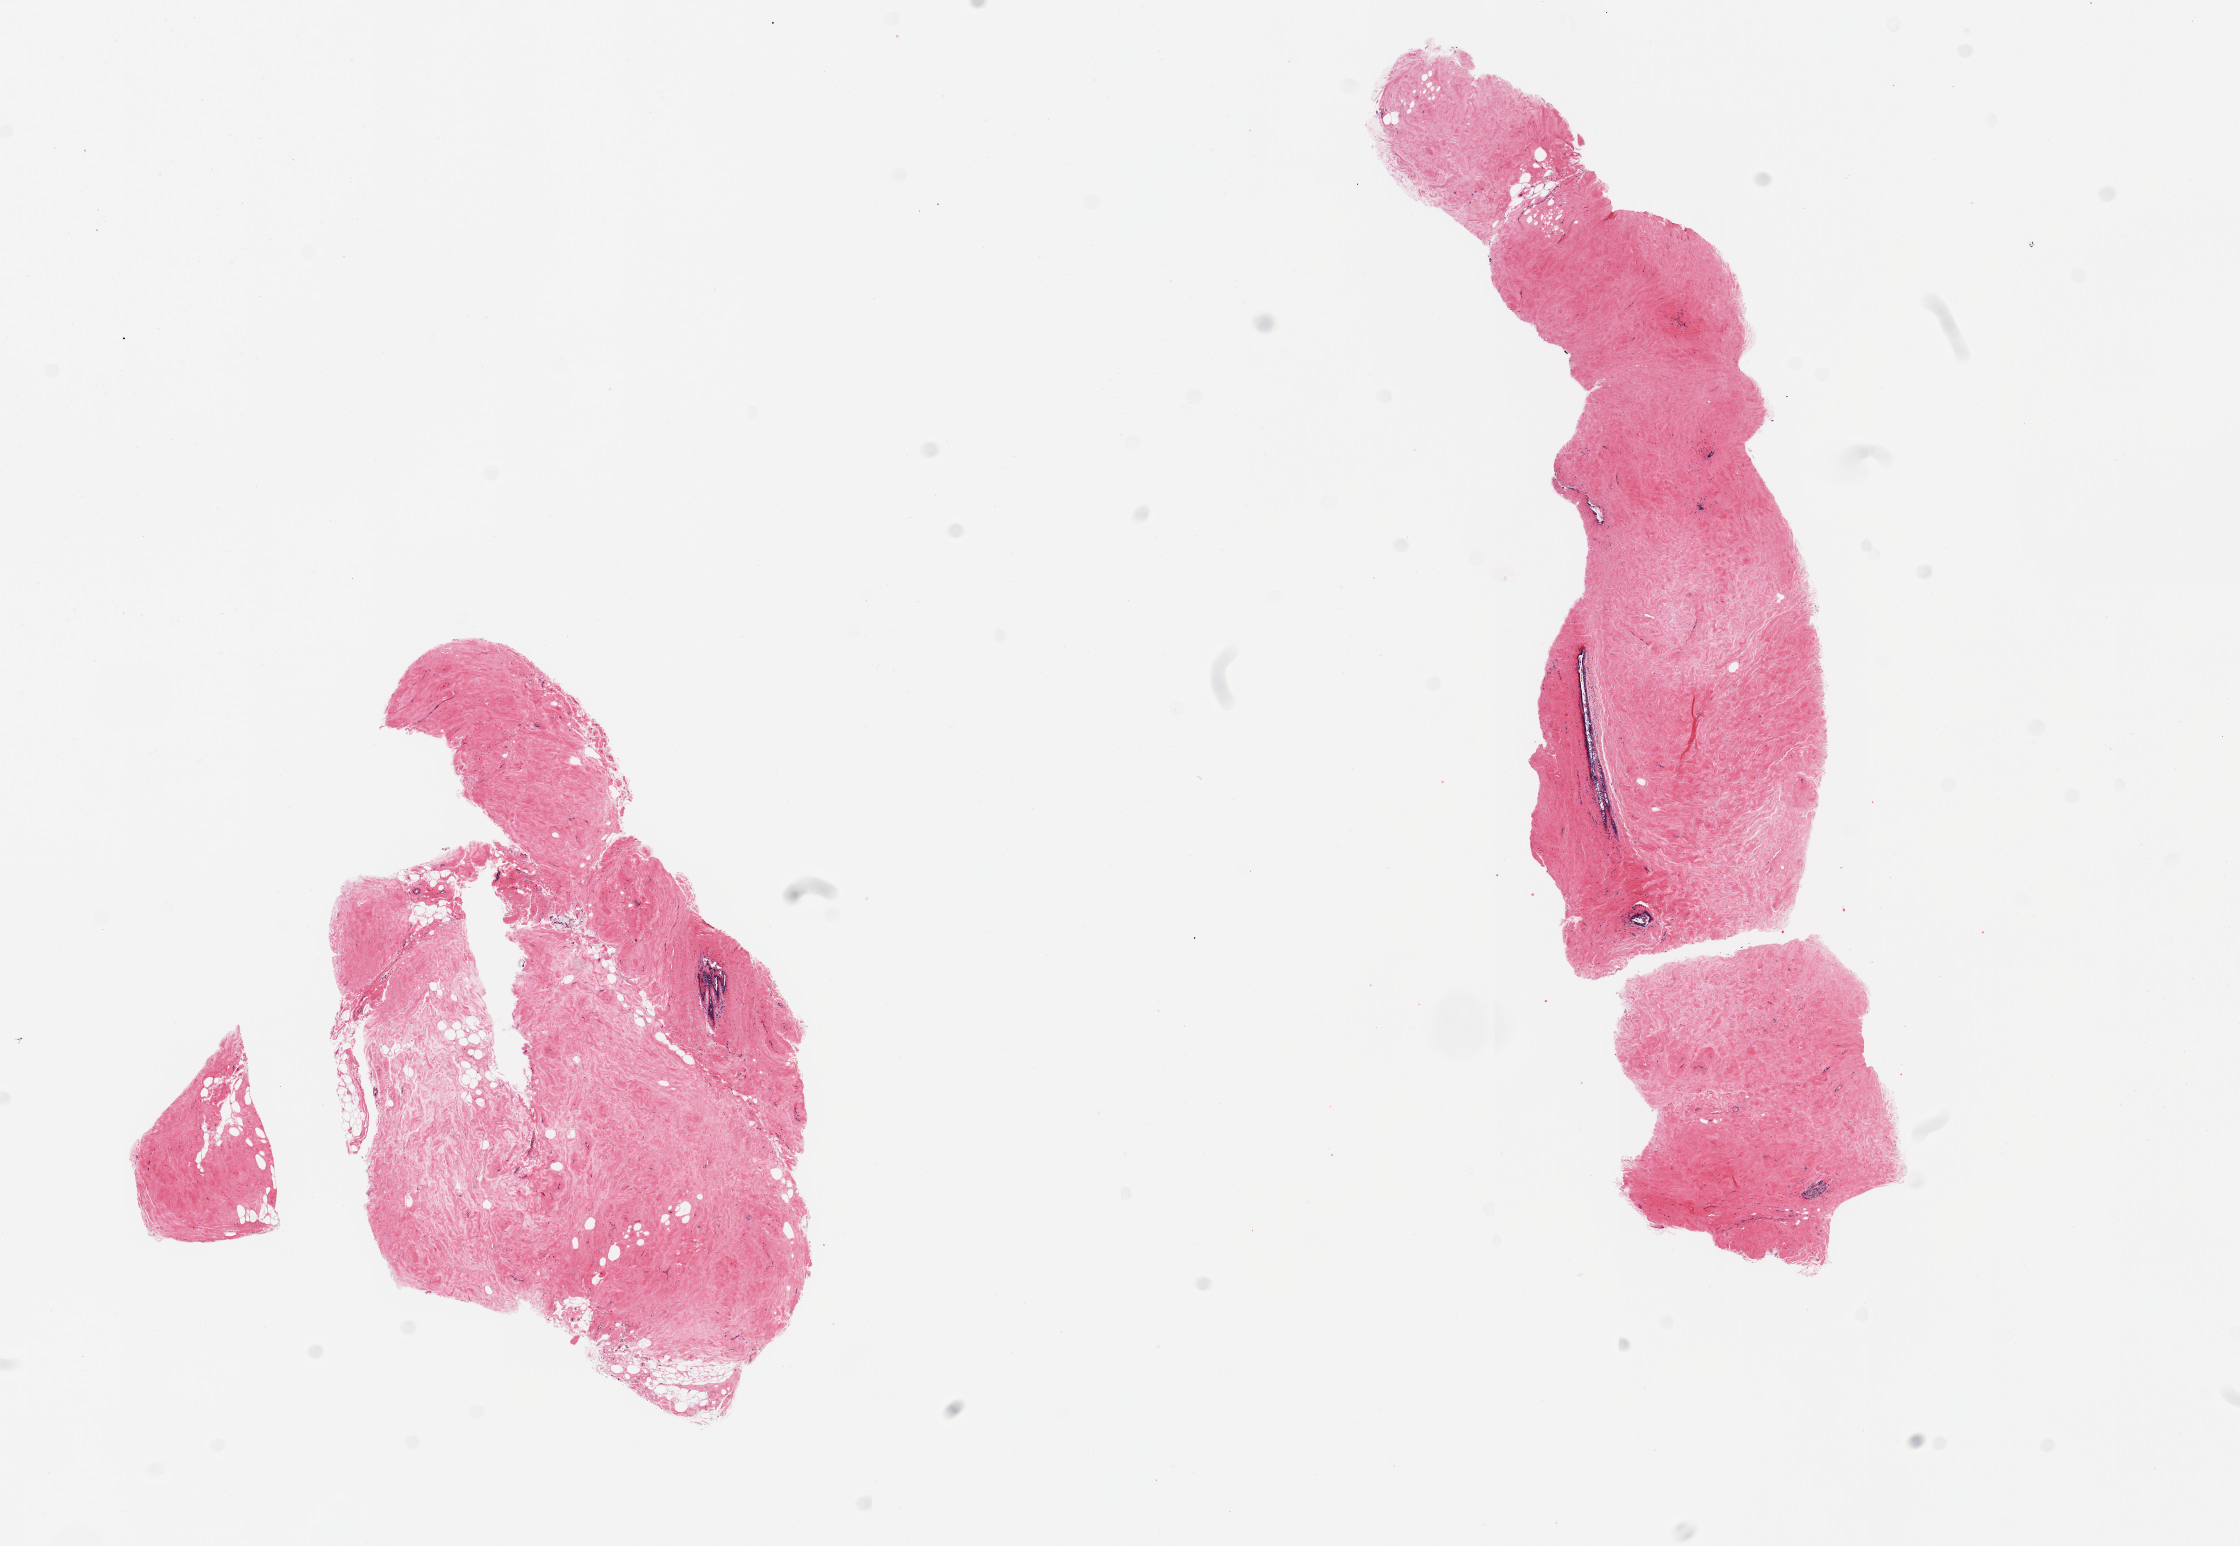
Digitized H&E-stained section, whole scanned area (about 17.7 x 12.2 mm) shown as a low-resolution overview, PAXgene-fixed paraffin-embedded (PFPE) section, sampled site (target tissue): breast, donor tissue sample.
Reviewer comment on this tissue sample: 2 pieces; fibrocollagenous stroma and few ducts.